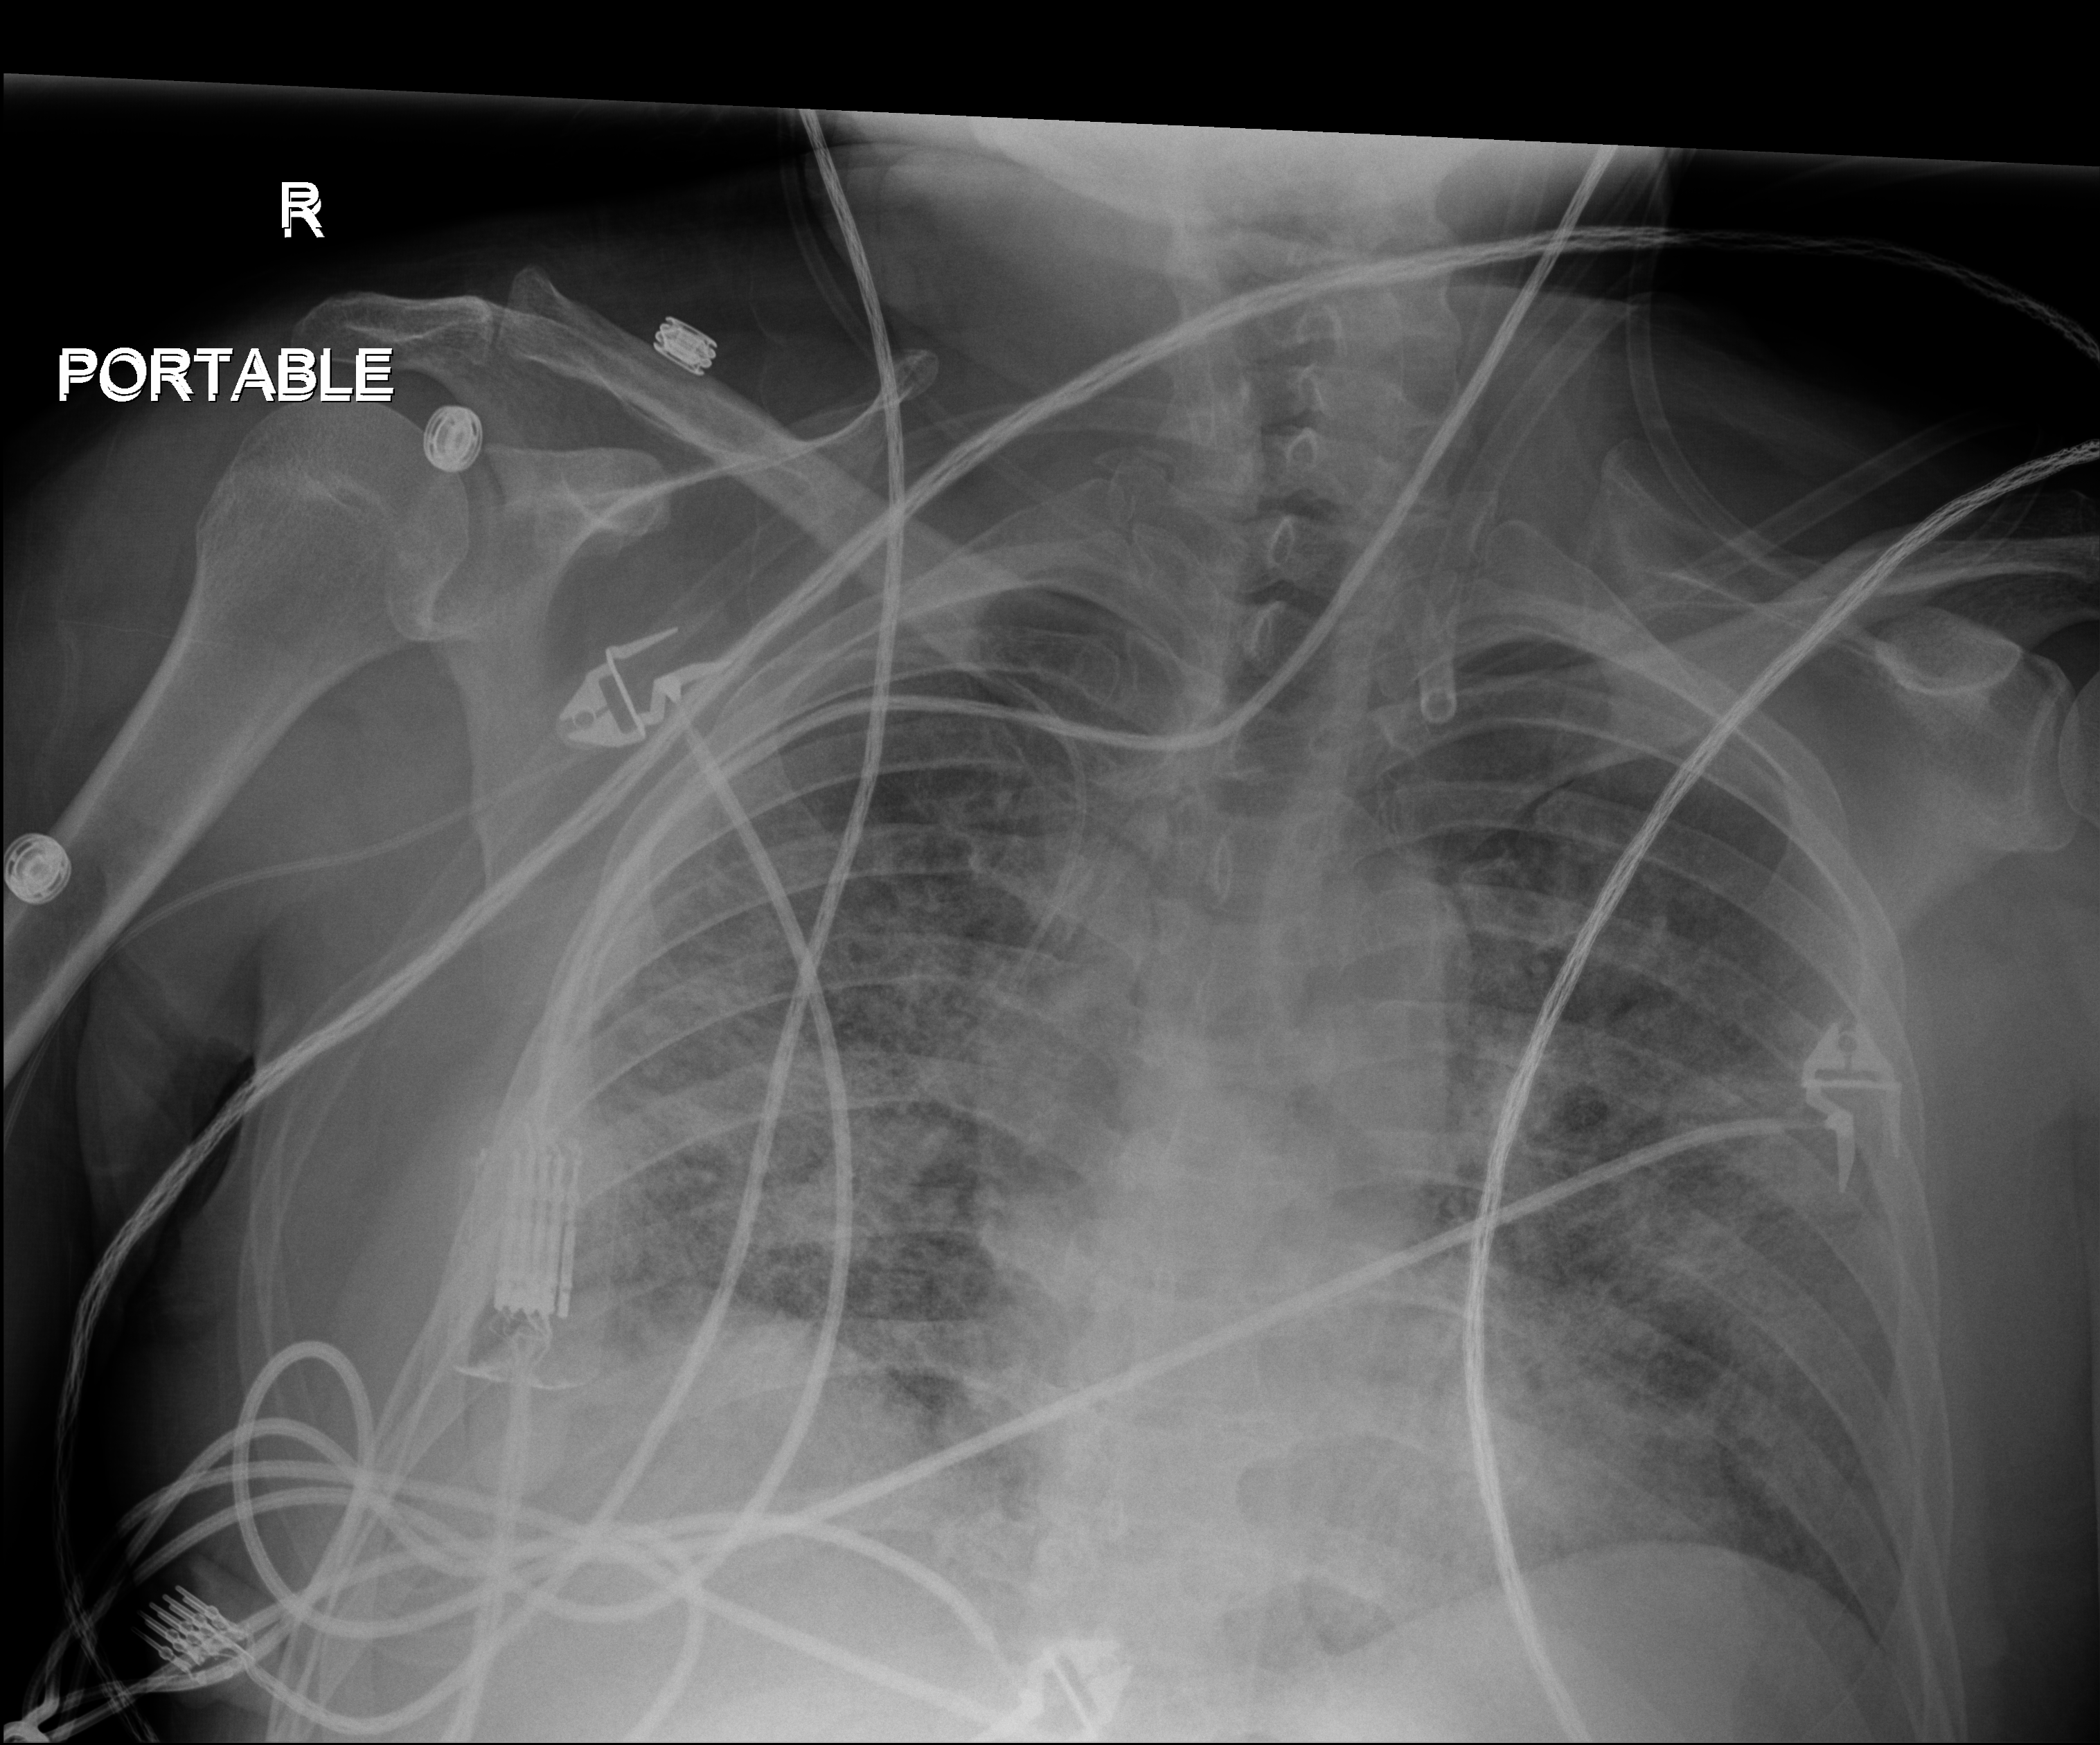
Chest X-ray. Male patient hospitalised with COVID-19, age 18–59 years.
From the hospital-stay record, not from the radiograph (when in the stay this image was taken is not recorded): chronic kidney disease (admission record): no; mechanically ventilated during this hospital stay: yes.